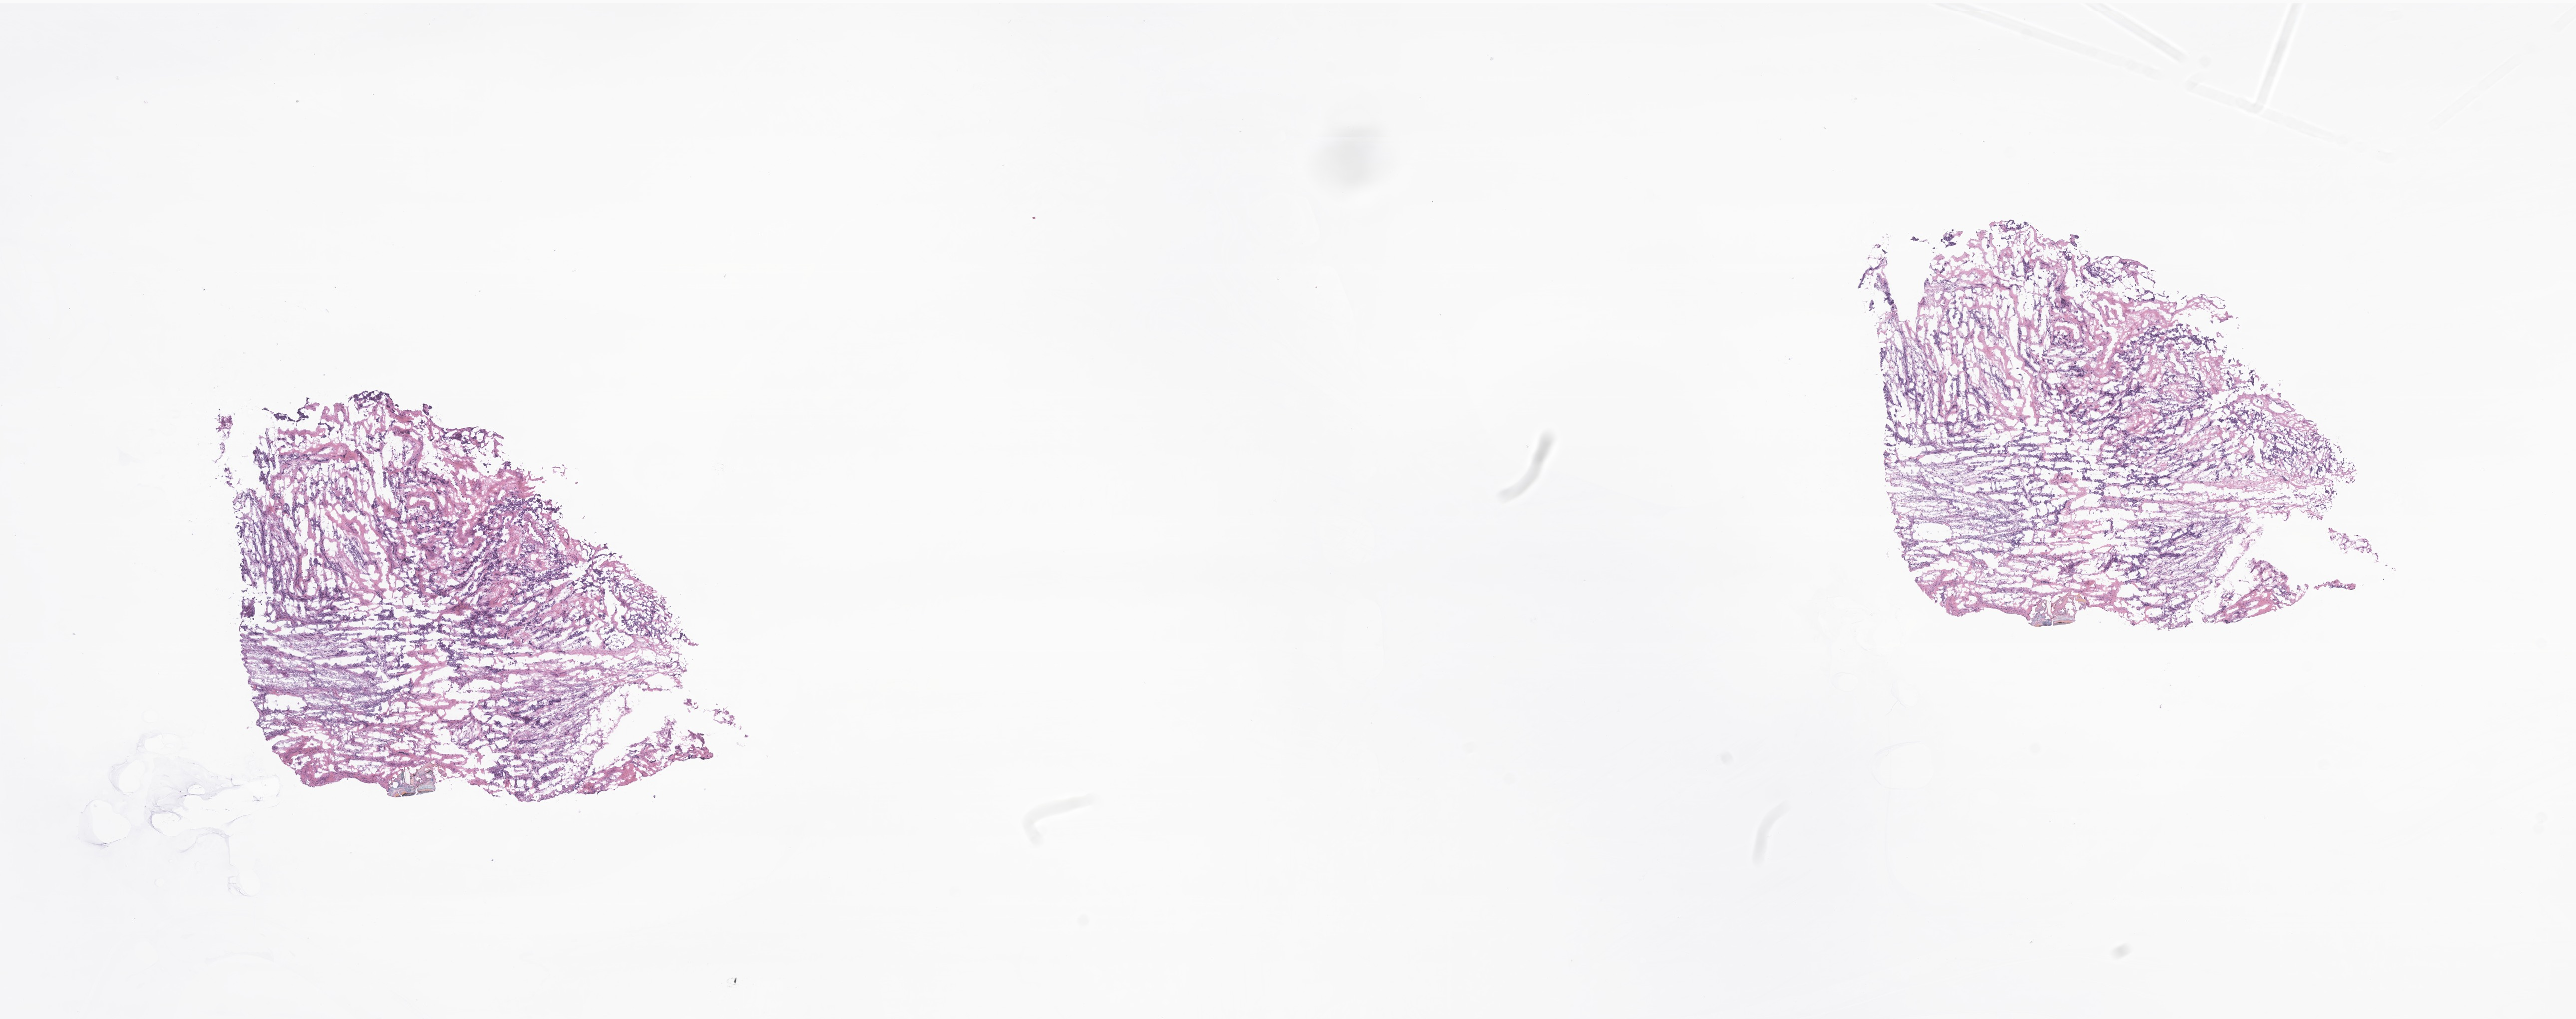
Whole-slide image, haematoxylin and eosin stain of tumor tissue from the abdomen, whole scanned area (about 21.8 x 8.6 mm) shown as a low-resolution overview, frozen section. Patient: male, age 204 months (17 years).
Recorded diagnosis: Alveolar rhabdomyosarcoma.